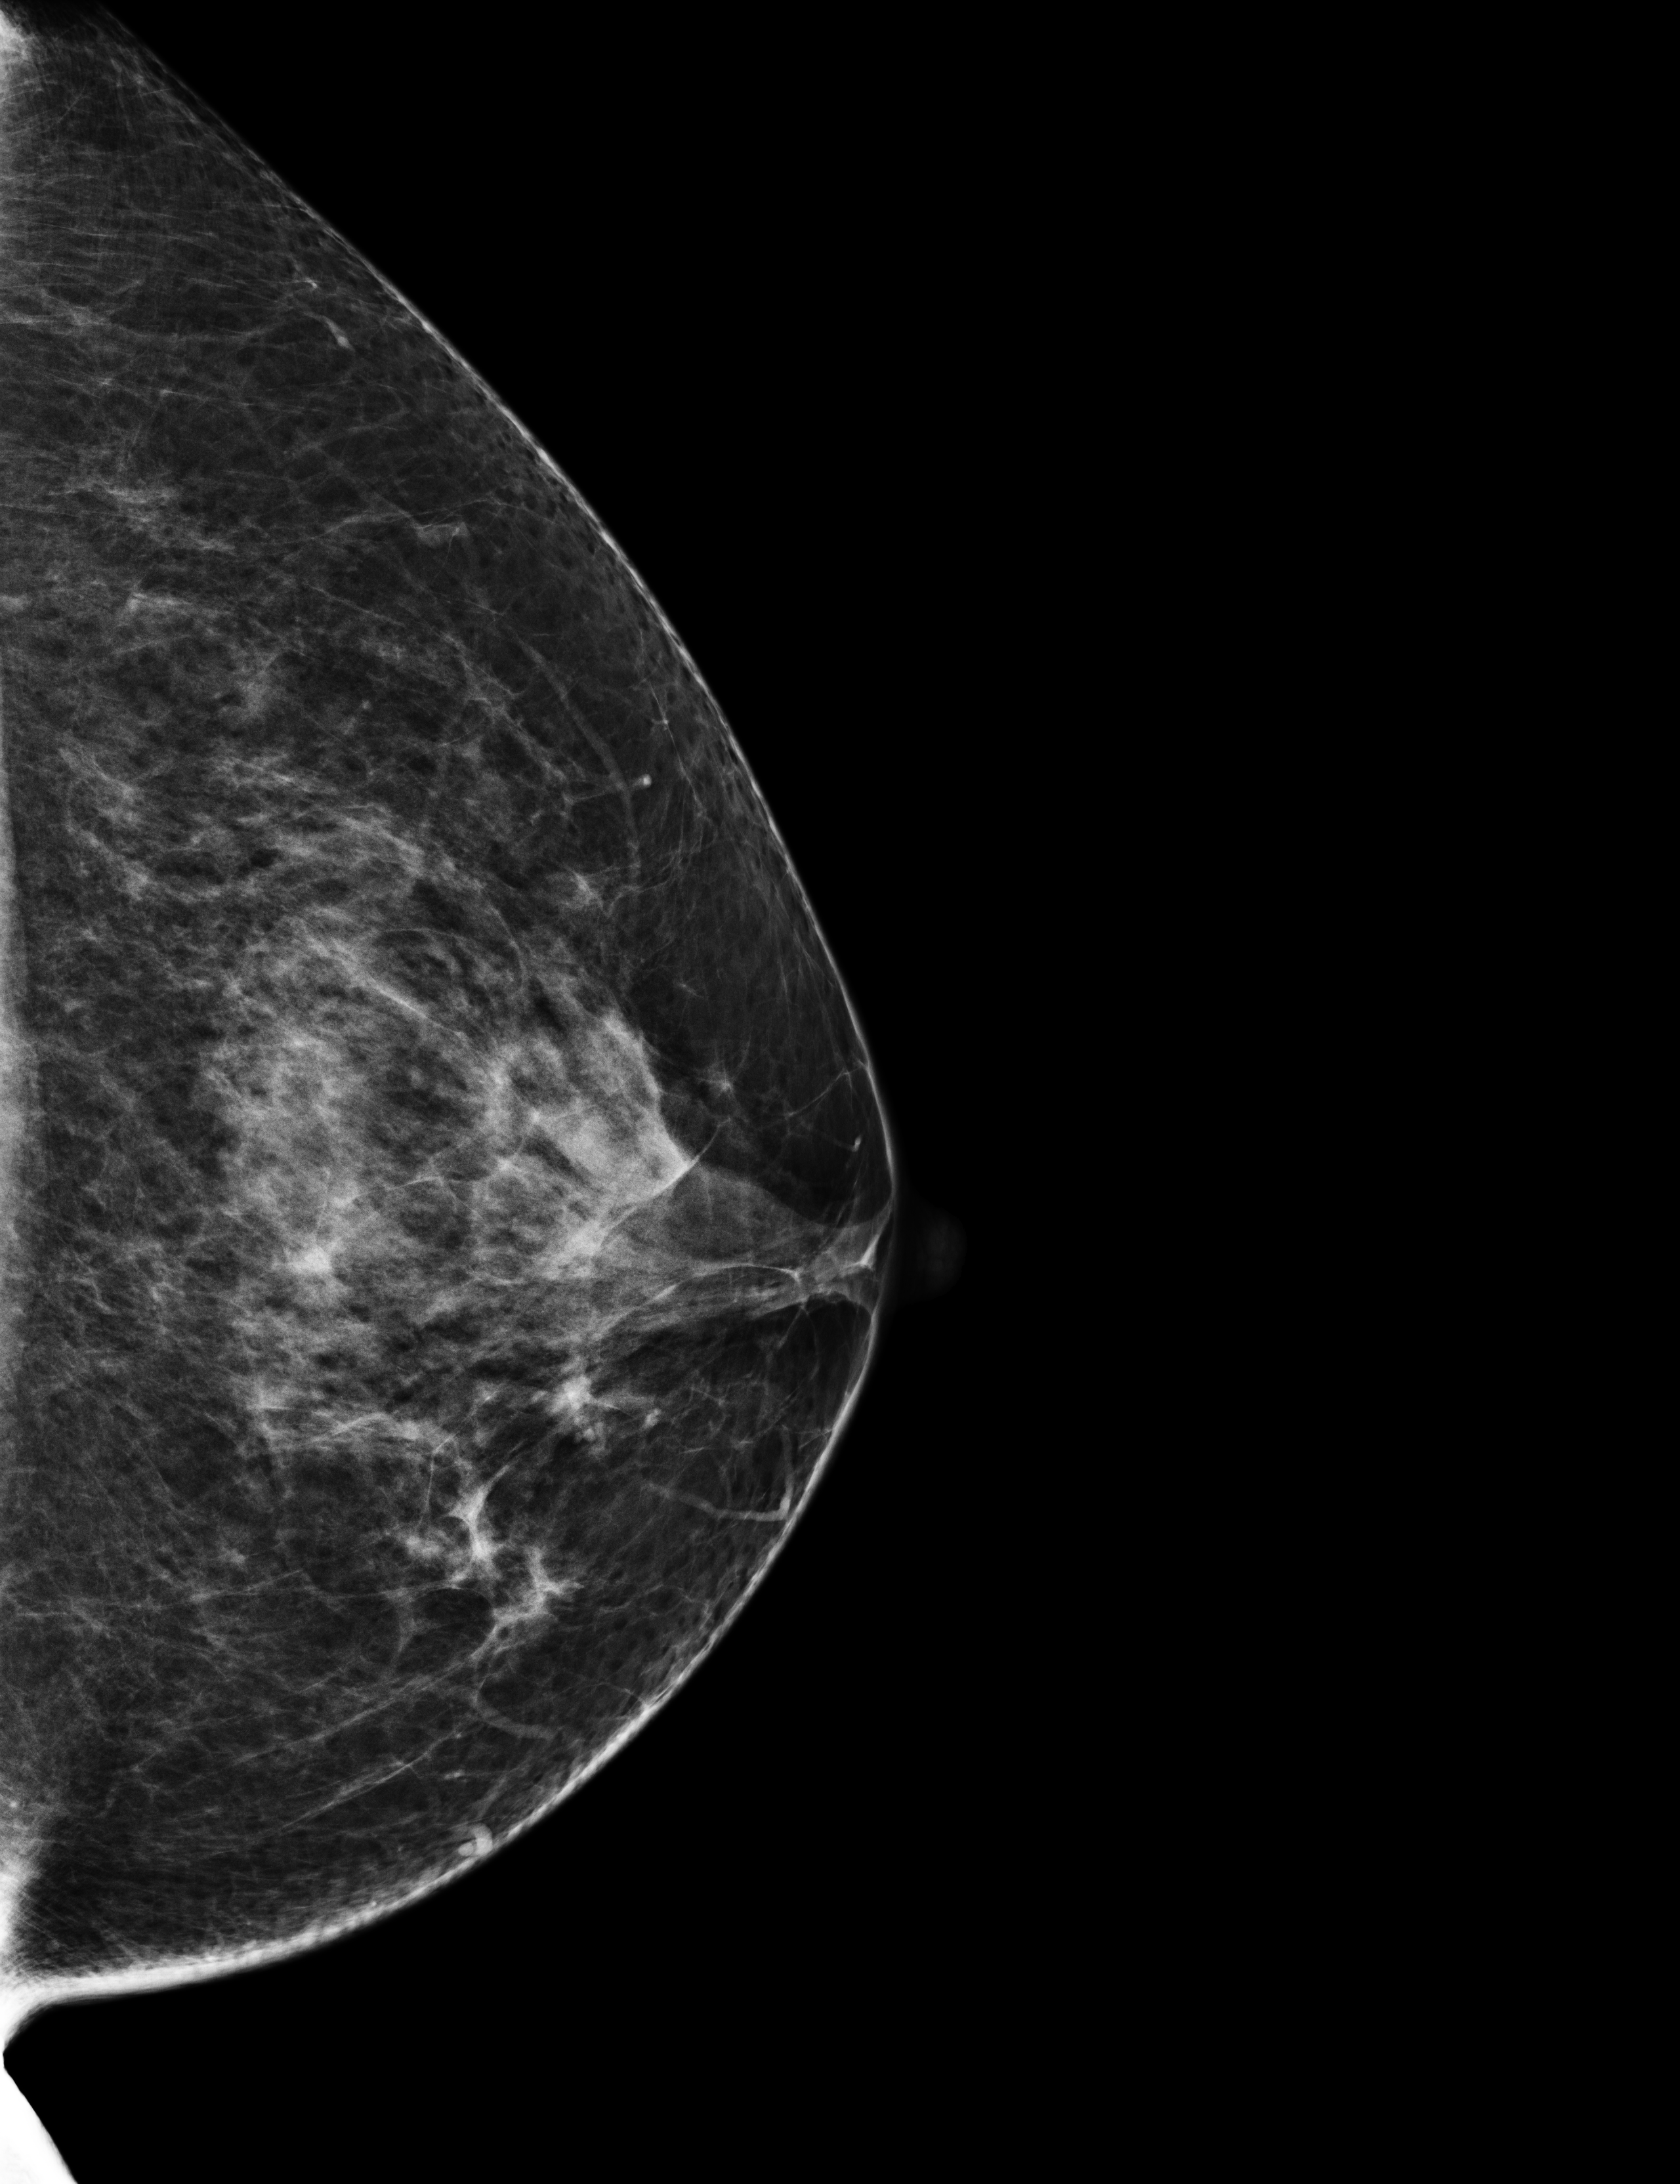
Annual screening mammography examination; compressed breast thickness 74 mm. Patient: female, 54 years.
Image type: full-field digital mammogram. Breast: left. Projection: CC view.